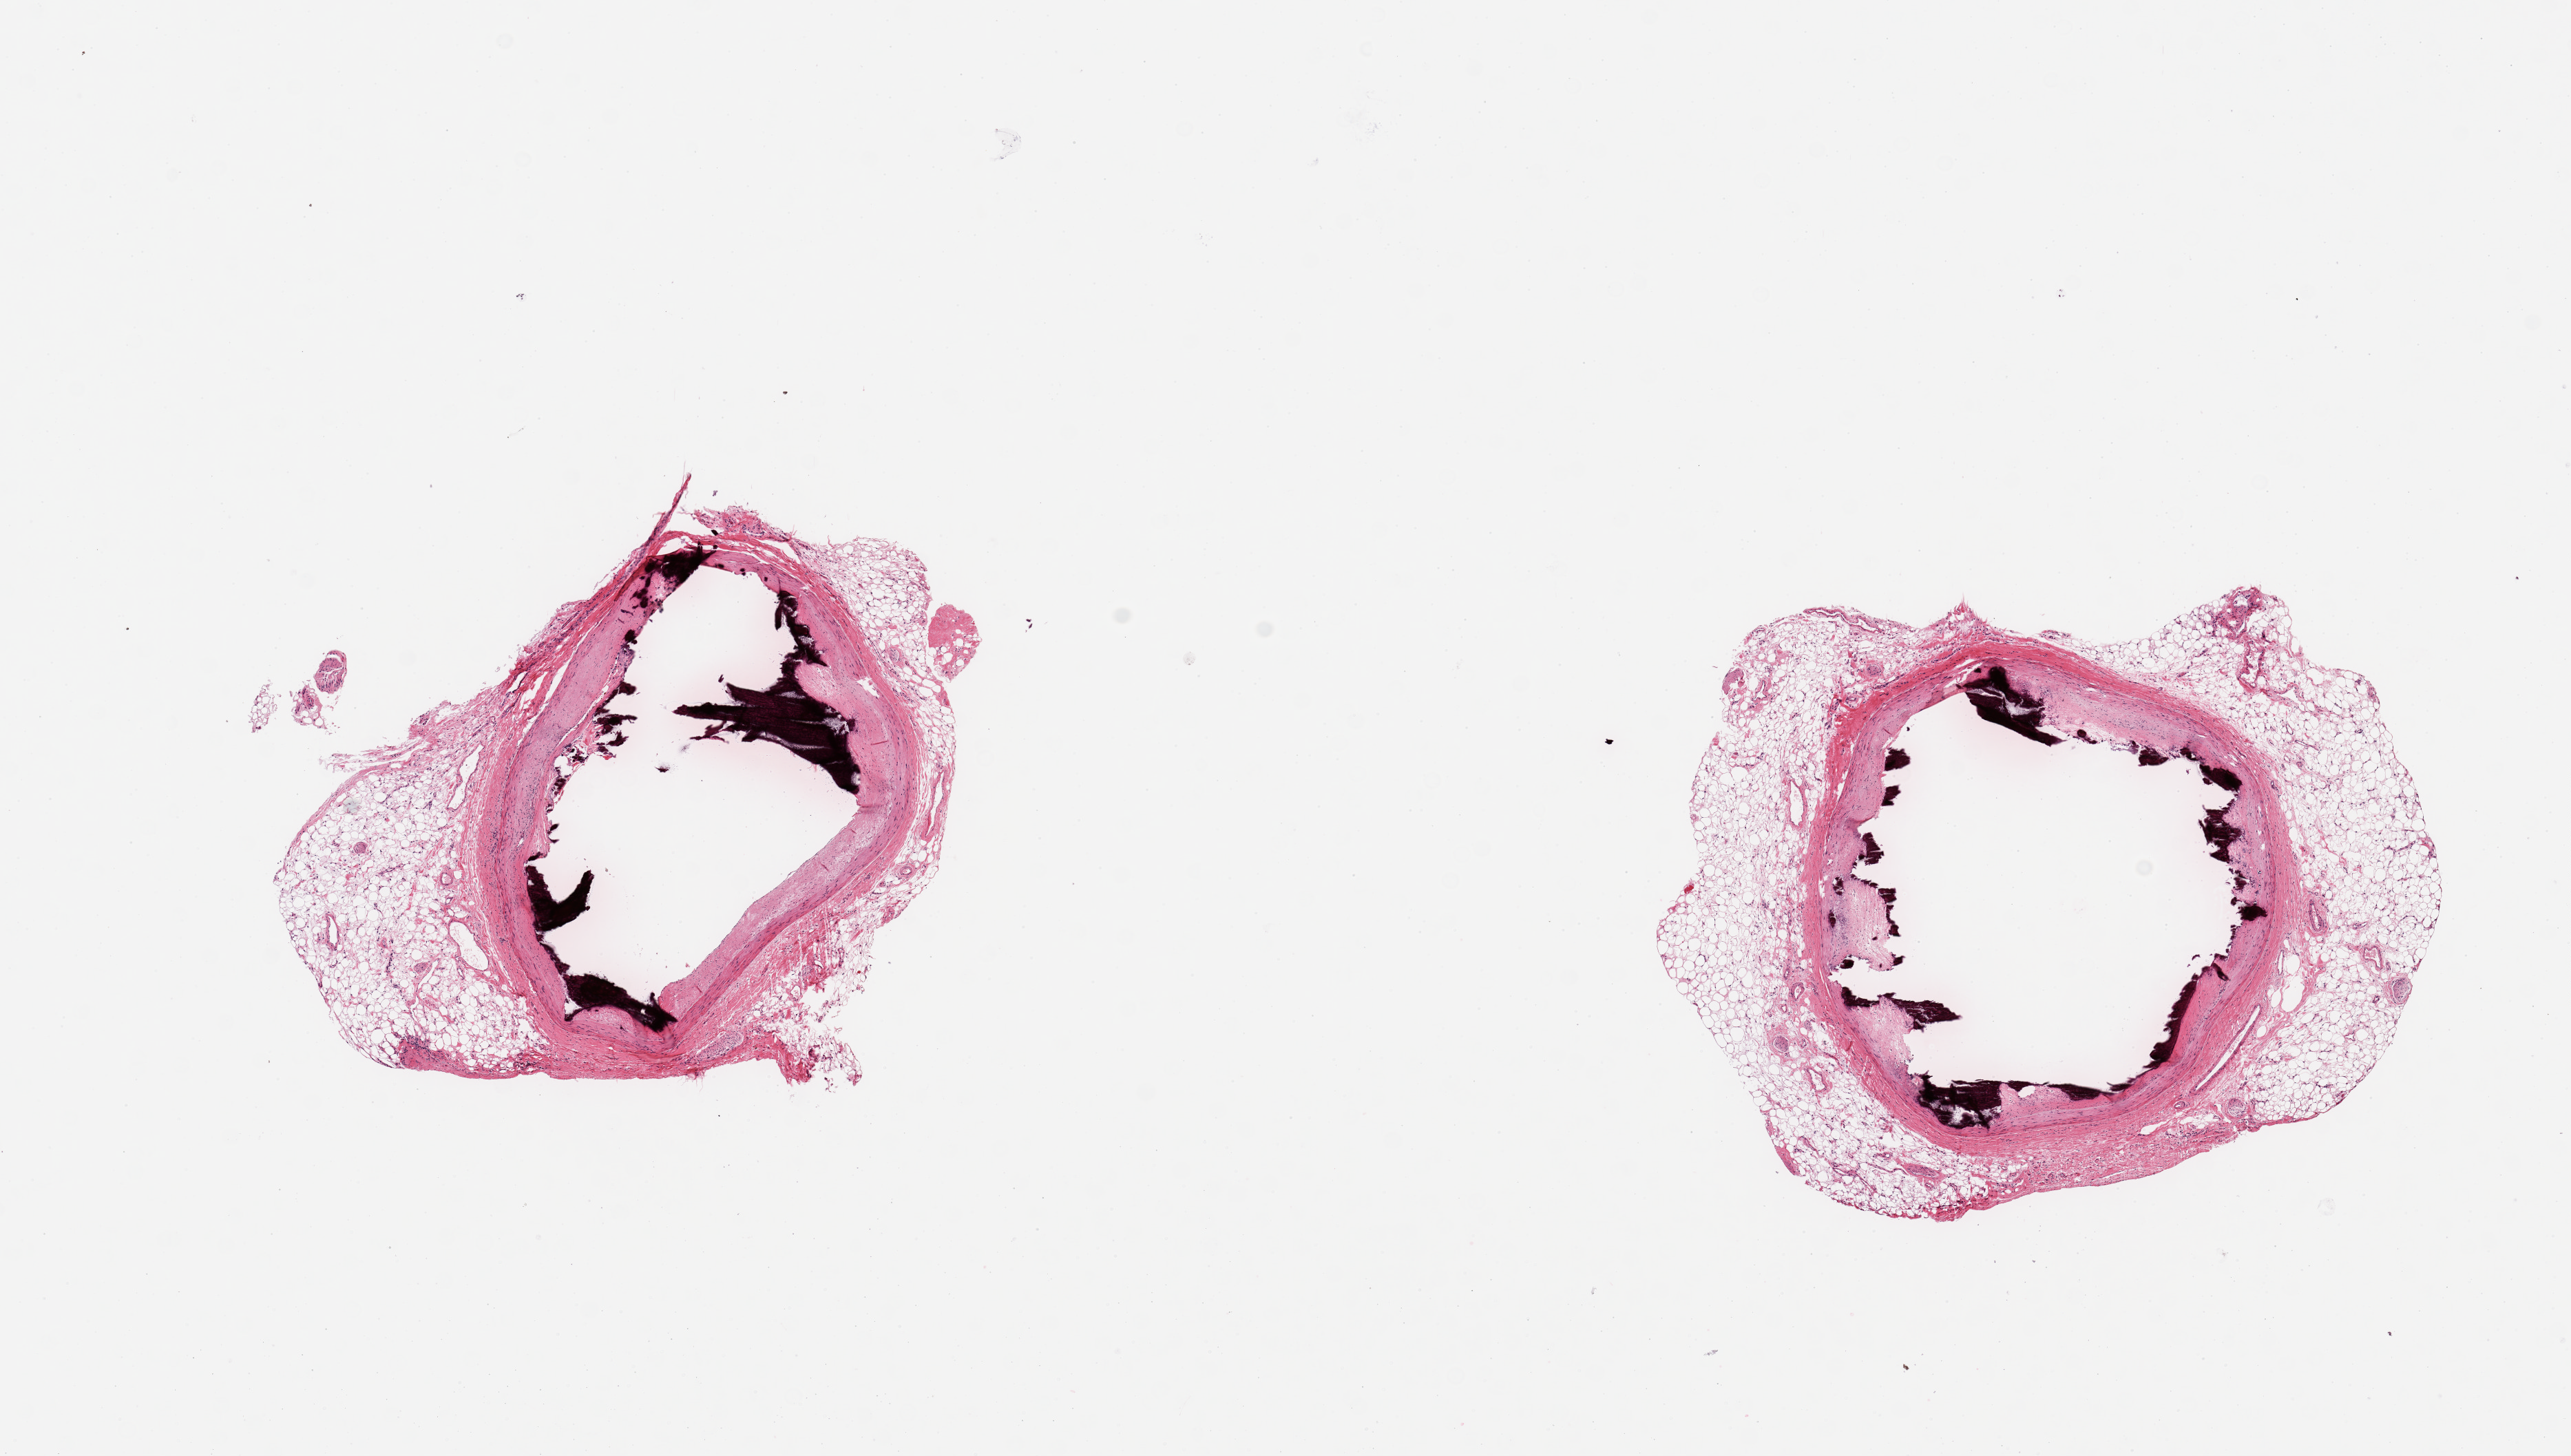
Digitized H&E-stained section — whole scanned area (about 14.8 x 8.4 mm) shown as a low-resolution overview. PAXgene-fixed paraffin-embedded (PFPE) section. Section of coronary artery (target tissue). Tissue donor sample.
Pathologist's review note for this sample: 2 pieces; heavily calcified atheromatous plaques; 50% external fat; minimal medial layer; limited value.